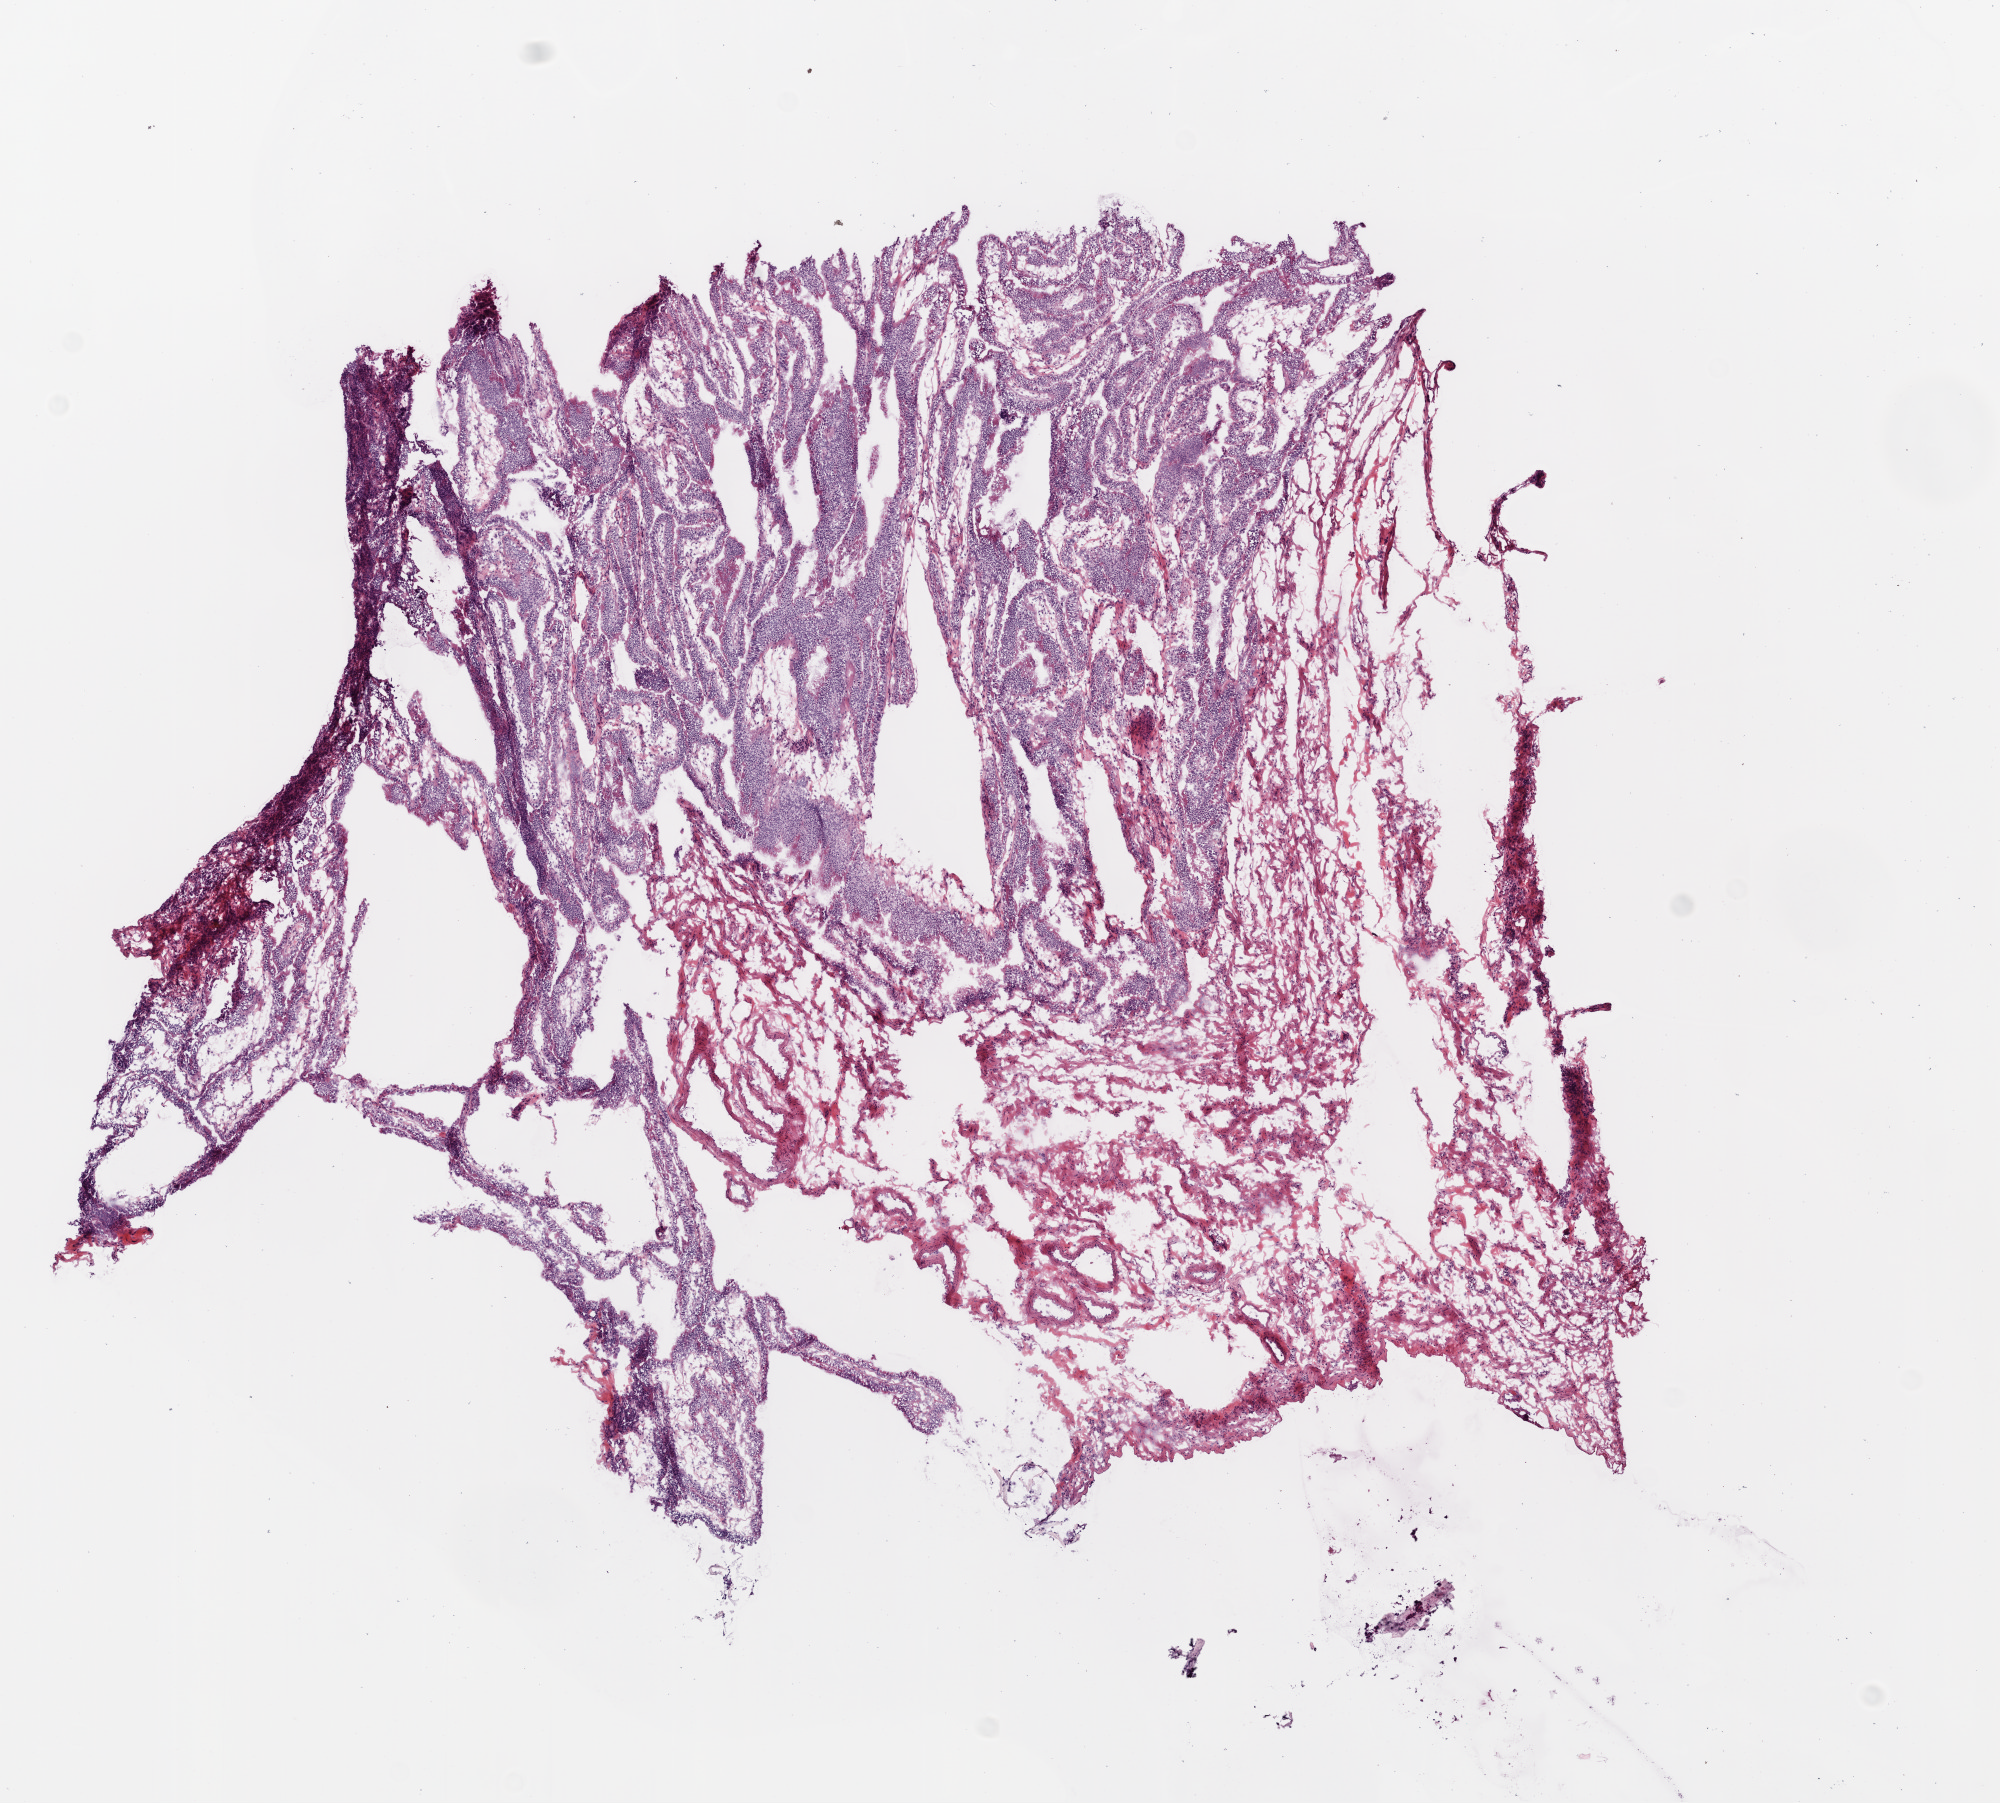
Hematoxylin and eosin (H&E) stained whole-slide image — a low-resolution overview of the entire scanned area, about 8.0 x 7.2 mm. Frozen section from the top of the tissue portion. Sample: solid tissue normal (non-tumour tissue), ovary. Patient: female, age at initial diagnosis 38 years.
- this section: solid tissue normal (non-tumour) sample from the same patient
- patient diagnosis: Serous cystadenocarcinoma, NOS